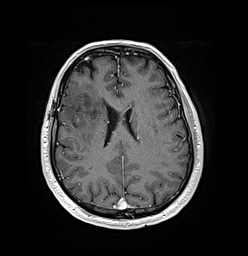
Brain MRI from a brain-tumour surgery series, one axial slice. Position 63 of 176 along the scan axis. T1-weighted post-contrast. 1 mm slice thickness. 248 × 256 image matrix, field of view 242 × 250 mm. Case-level facts recorded for this patient, not image findings: histopathology: Oligodendroglioma; WHO grade: 3; IDH mutation: yes; tumour location: Right Frontal.
Structures marked on this image (expert manual segmentation):
- tumour: bounding box (x1, y1, x2, y2) in pixels: (74, 116, 82, 124)